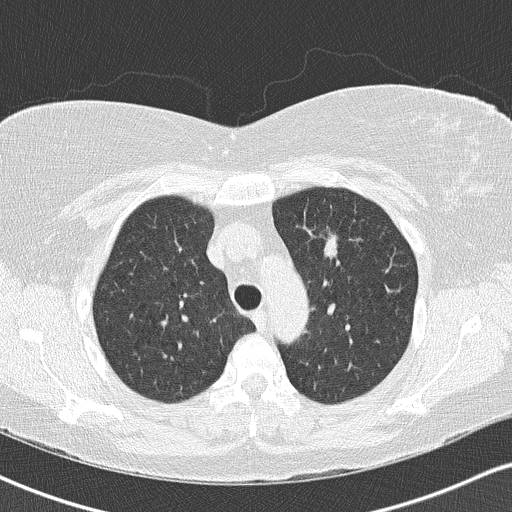
Axial slice from a low-dose chest CT screening exam. Second screening round (one year after baseline). Lung window (W 1500 / L -600 HU). 2 mm slice thickness. Lung (sharp) reconstruction kernel (B50f). 512 × 512 image matrix, field of view 328 × 328 mm. Female participant, aged 57 years at enrolment.
Expert-annotated lung lesion, bounding box (x1, y1, x2, y2) in pixels: (313, 224, 349, 266). The screening reader recorded 3 non-calcified nodules or masses ≥4 mm on this exam (left upper lobe, right upper lobe, right middle lobe); which of them this box marks is not recorded. Official screen result: positive, other. Later outcome: lung cancer diagnosed 75 days after this screen — adenocarcinoma, NOS, left upper lobe, poorly differentiated (G3), stage IA (AJCC 6th edition), 24 mm at pathology.